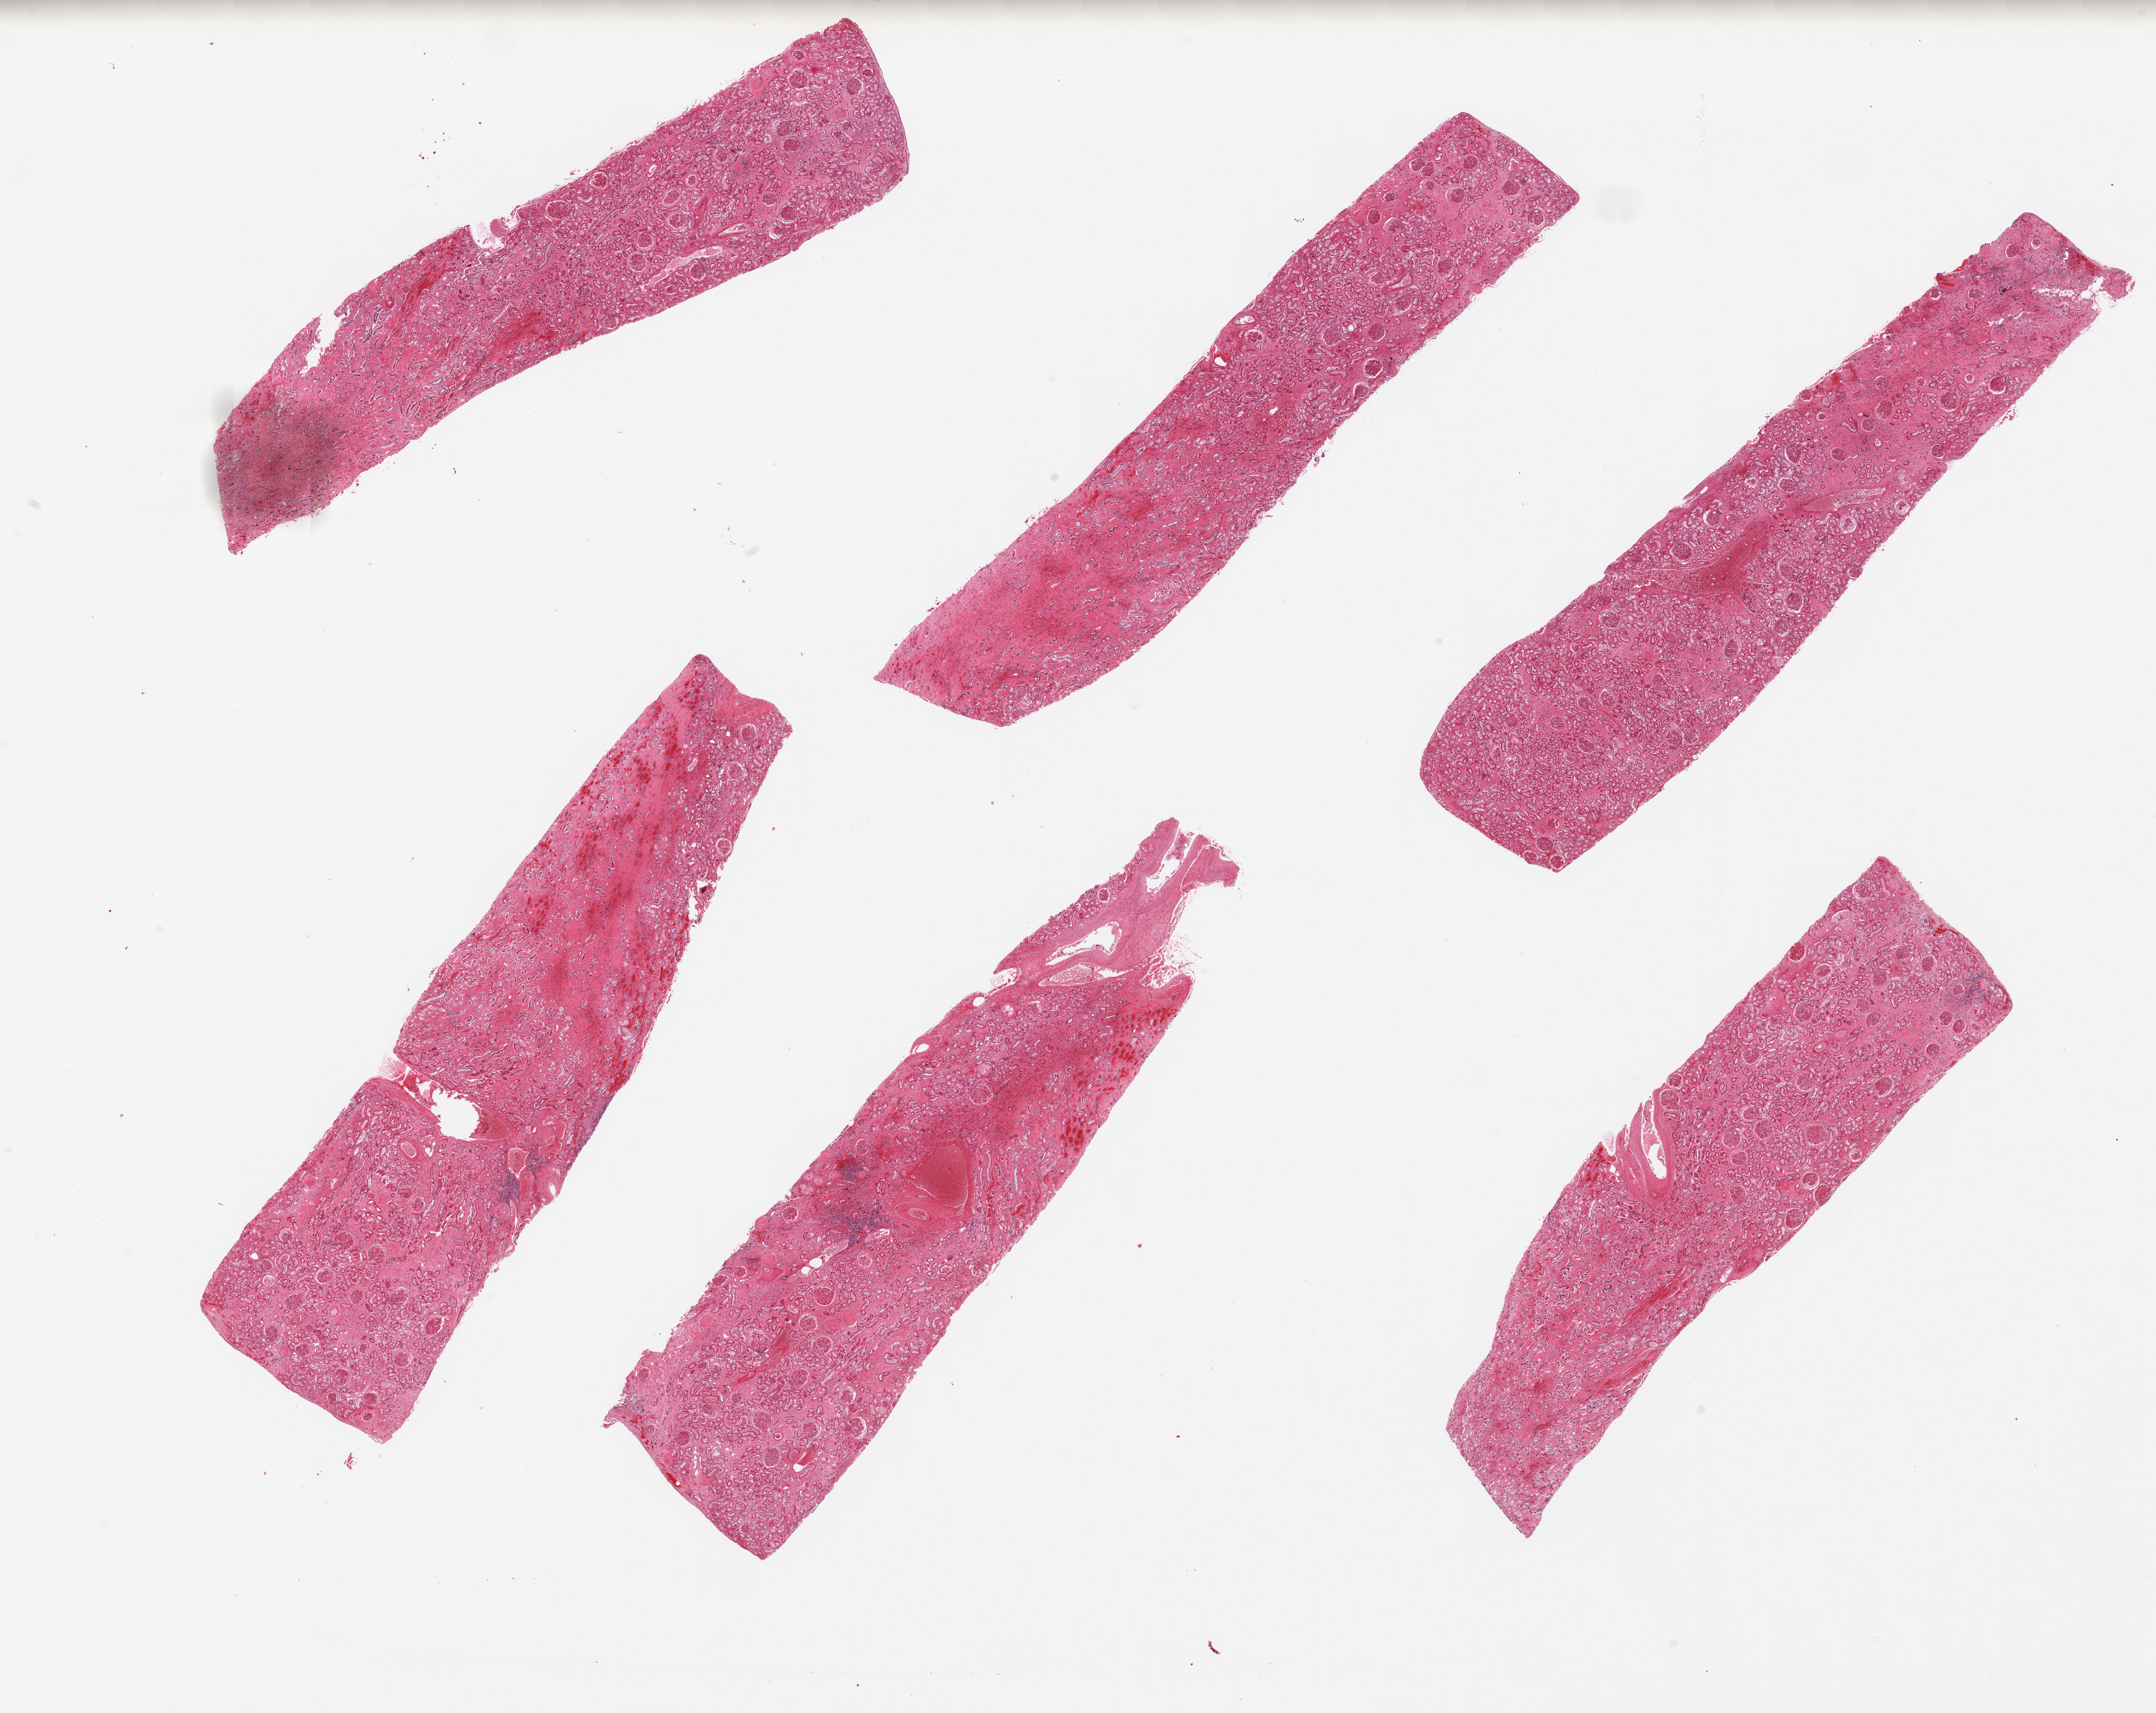
Digitized H&E-stained section — shown as a low-resolution overview of the whole scanned area (about 27.6 x 21.9 mm, from a 20x scan), PAXgene-fixed paraffin-embedded (PFPE) section, sampled site (target tissue): renal cortex, tissue donor sample. Donor sex: male.
- review note (as recorded): 6 pieces, glomeruli present but markedly autolyzed